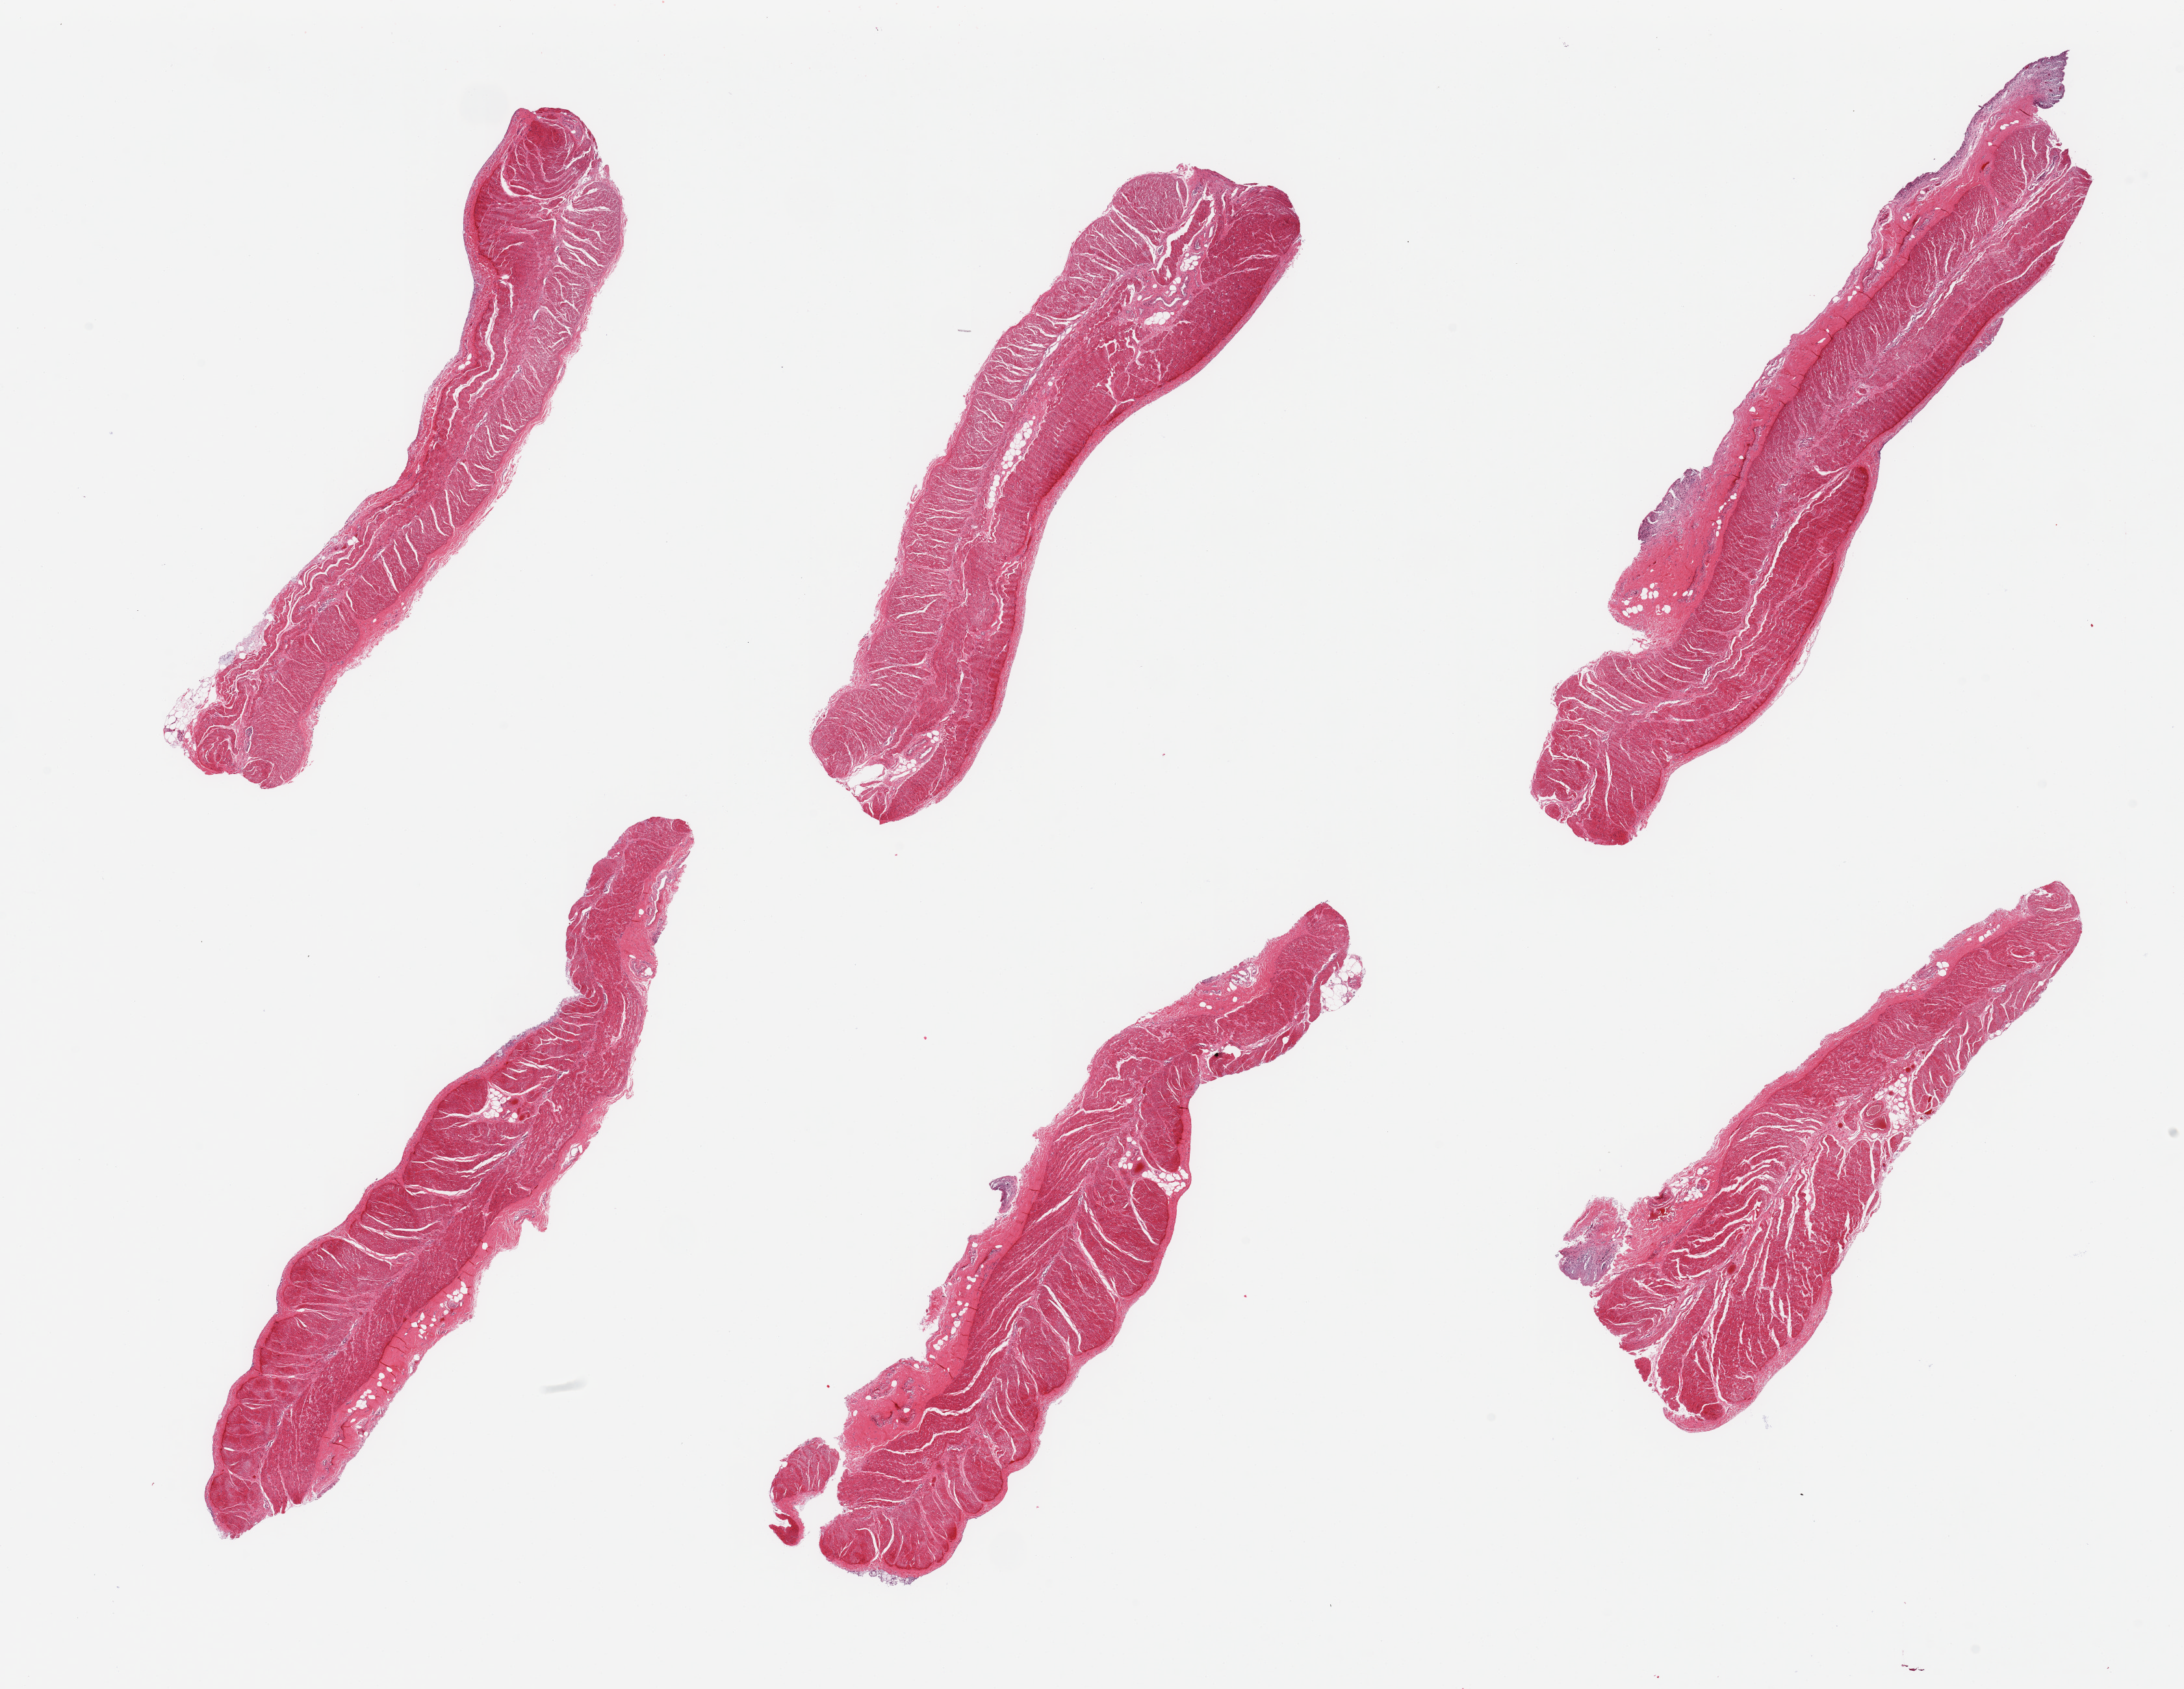
Whole-slide image, haematoxylin and eosin stain — whole scanned area (about 26.6 x 20.6 mm, slide scanned at 20x) shown as a low-resolution overview, PAXgene-fixed paraffin-embedded (PFPE) section, sampled site (target tissue): sigmoid colon, tissue donor sample.
- reviewer comment on this tissue sample: 6 pieces, confirmed target muscularis